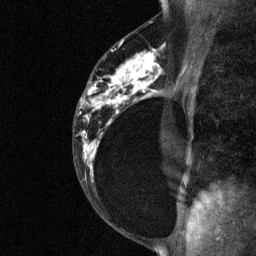
Breast MRI (dynamic contrast-enhanced), one sagittal slice. Position 40 of 64 along the scan axis. Dynamic contrast-enhanced study with each time point stored as its own series, time point 2 of 3 at this slice position (early post-contrast, ordered by acquisition time). 1.5 T. TE 4.8 ms, TR 27 ms. 256 × 256 image matrix. Patient: female, 34 years. Case-level facts recorded for this patient, not image findings: setting: breast cancer imaged before/during neoadjuvant chemotherapy; receptor status: HR-positive, HER2-negative.
Outlined on this slice (semi-automatic segmentation, software-assisted and operator-edited):
- analysis volume of interest (the breast-tissue region the enhancement analysis was run in; not a lesion): bounding box (x1, y1, x2, y2) in pixels: (78, 44, 181, 191)
- tumour enhancement mask (voxels above the 90 % enhancement threshold inside the analysis volume of interest): (84, 52, 161, 169)